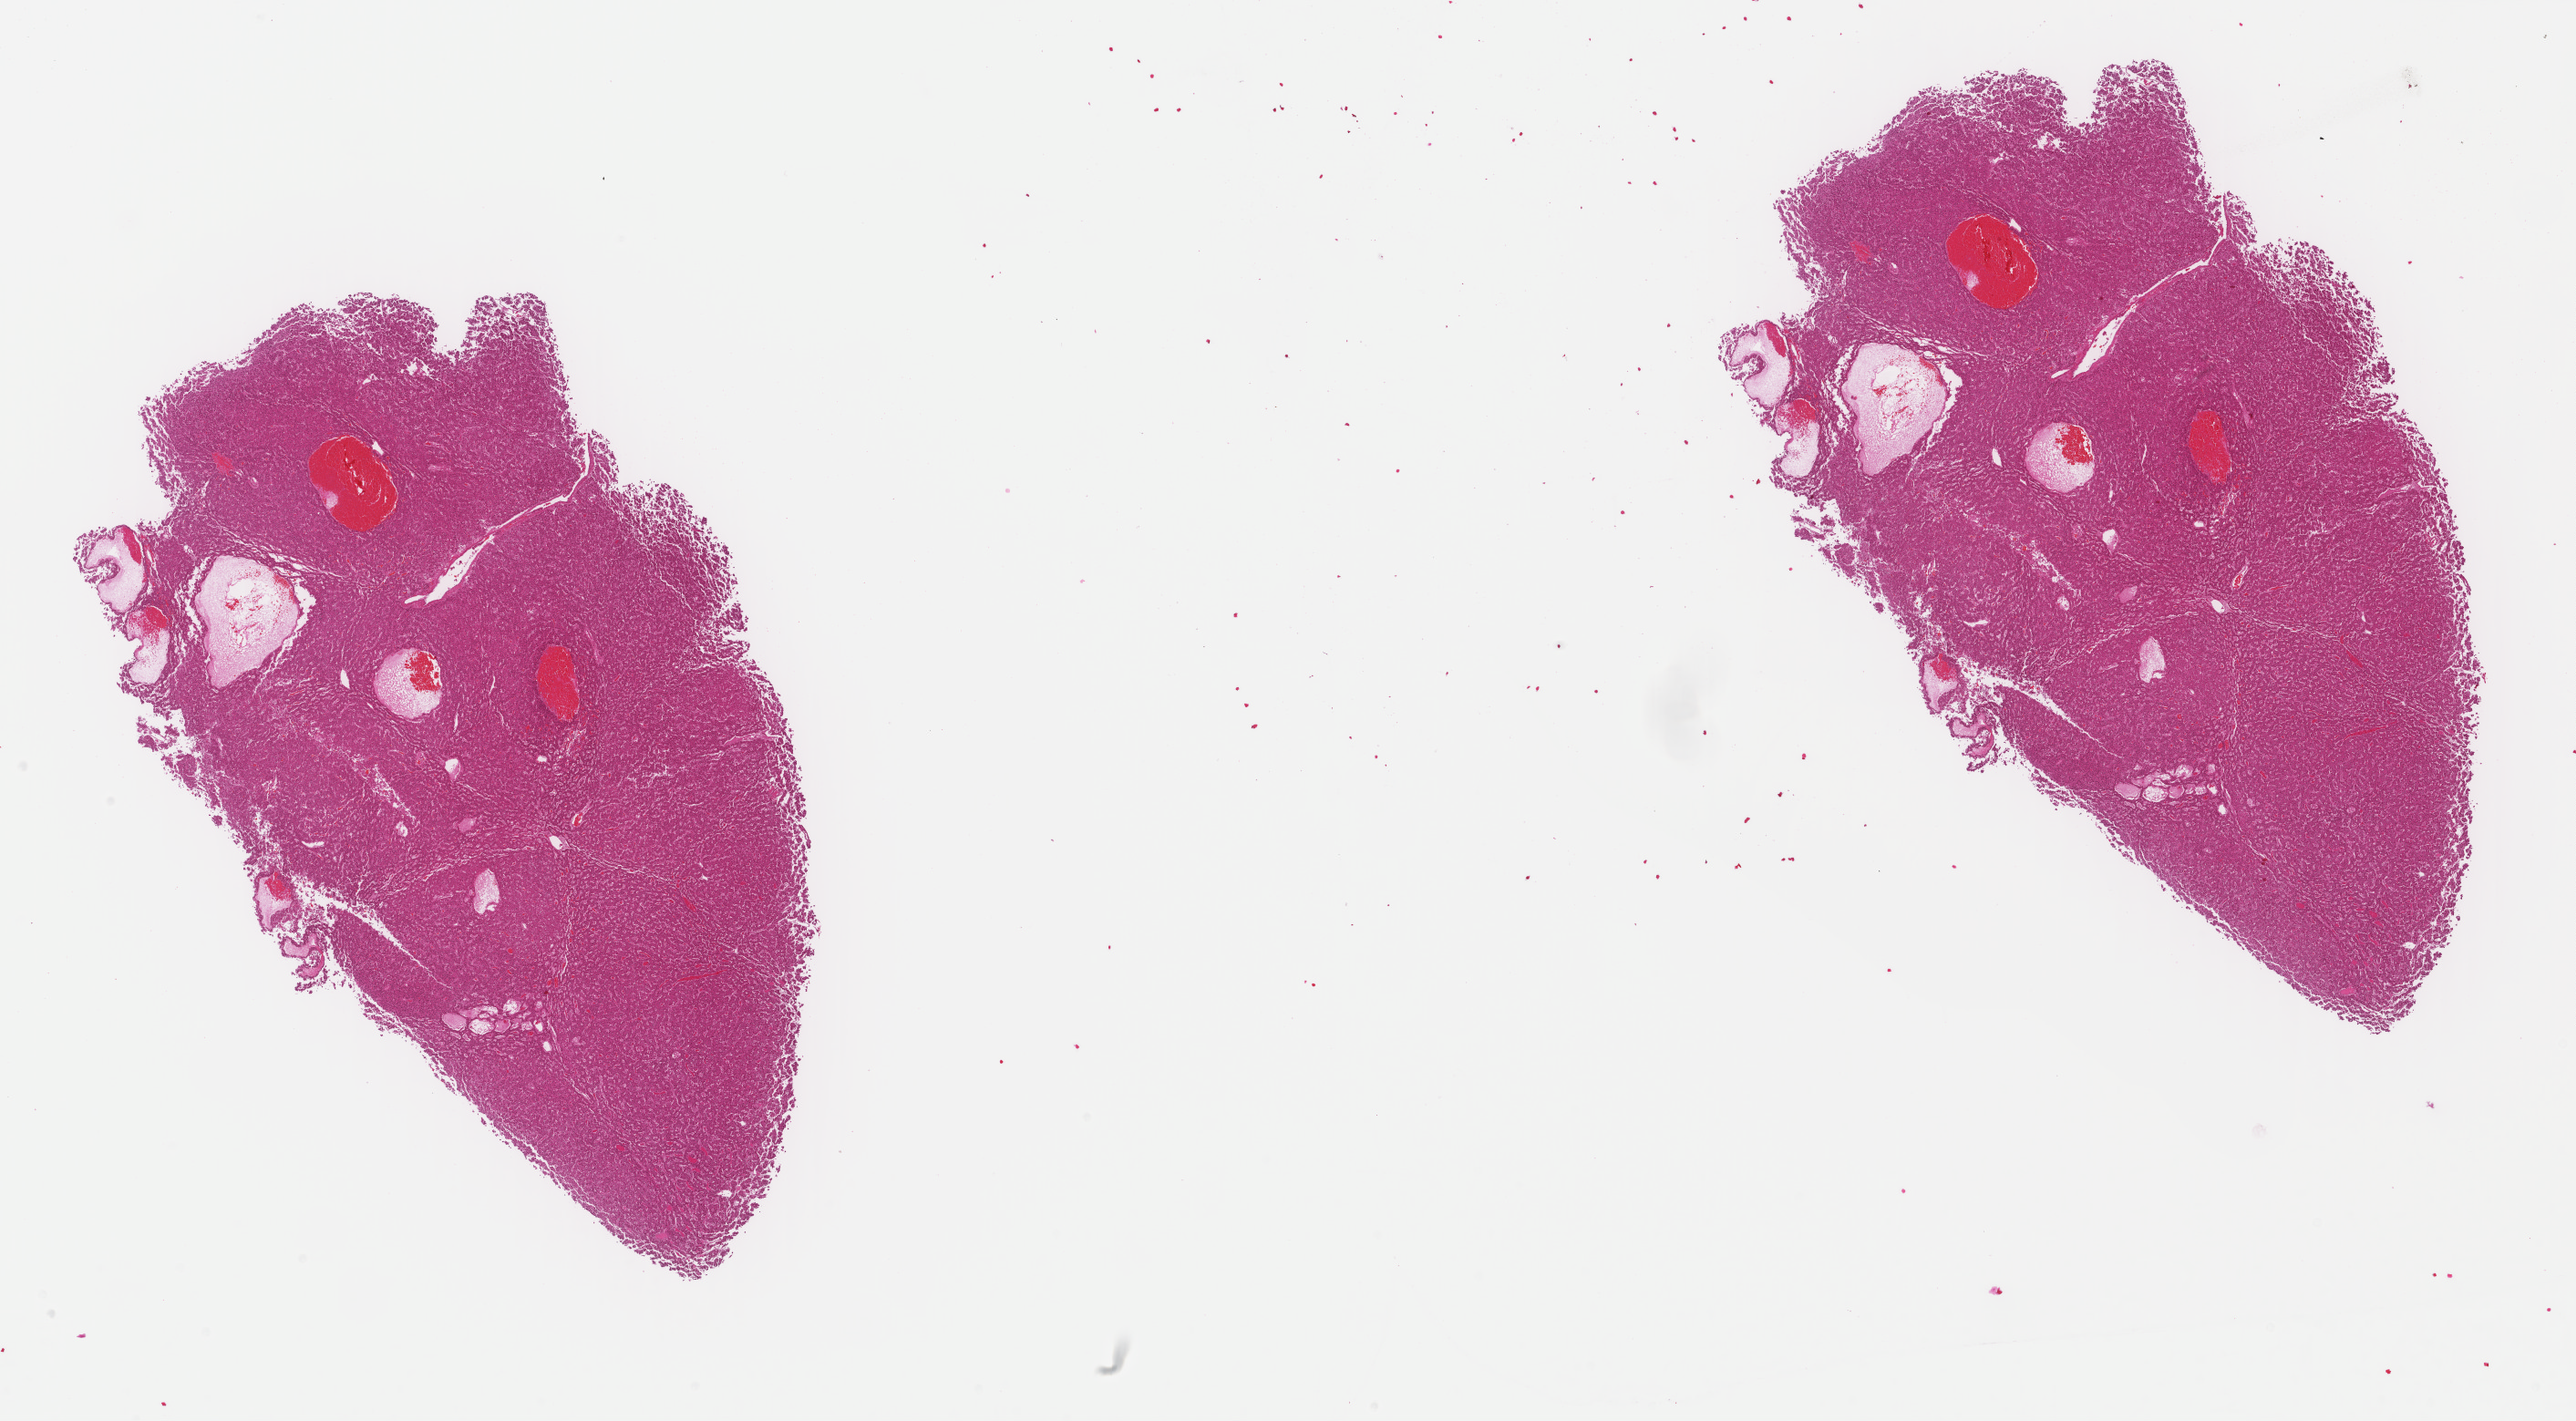
Whole-slide histology image, H&E-stained, low-resolution overview of the scanned area, about 22.4 x 12.4 mm (slide scanned at 40x). Formalin-fixed paraffin-embedded (FFPE) diagnostic section. Primary tumour sample from the liver. Patient: female, age at initial diagnosis 62 years. Histologic grade: G2 (moderately differentiated).
* AJCC pathologic stage: I (6th edition)
* histologic diagnosis: Hepatocellular carcinoma, NOS